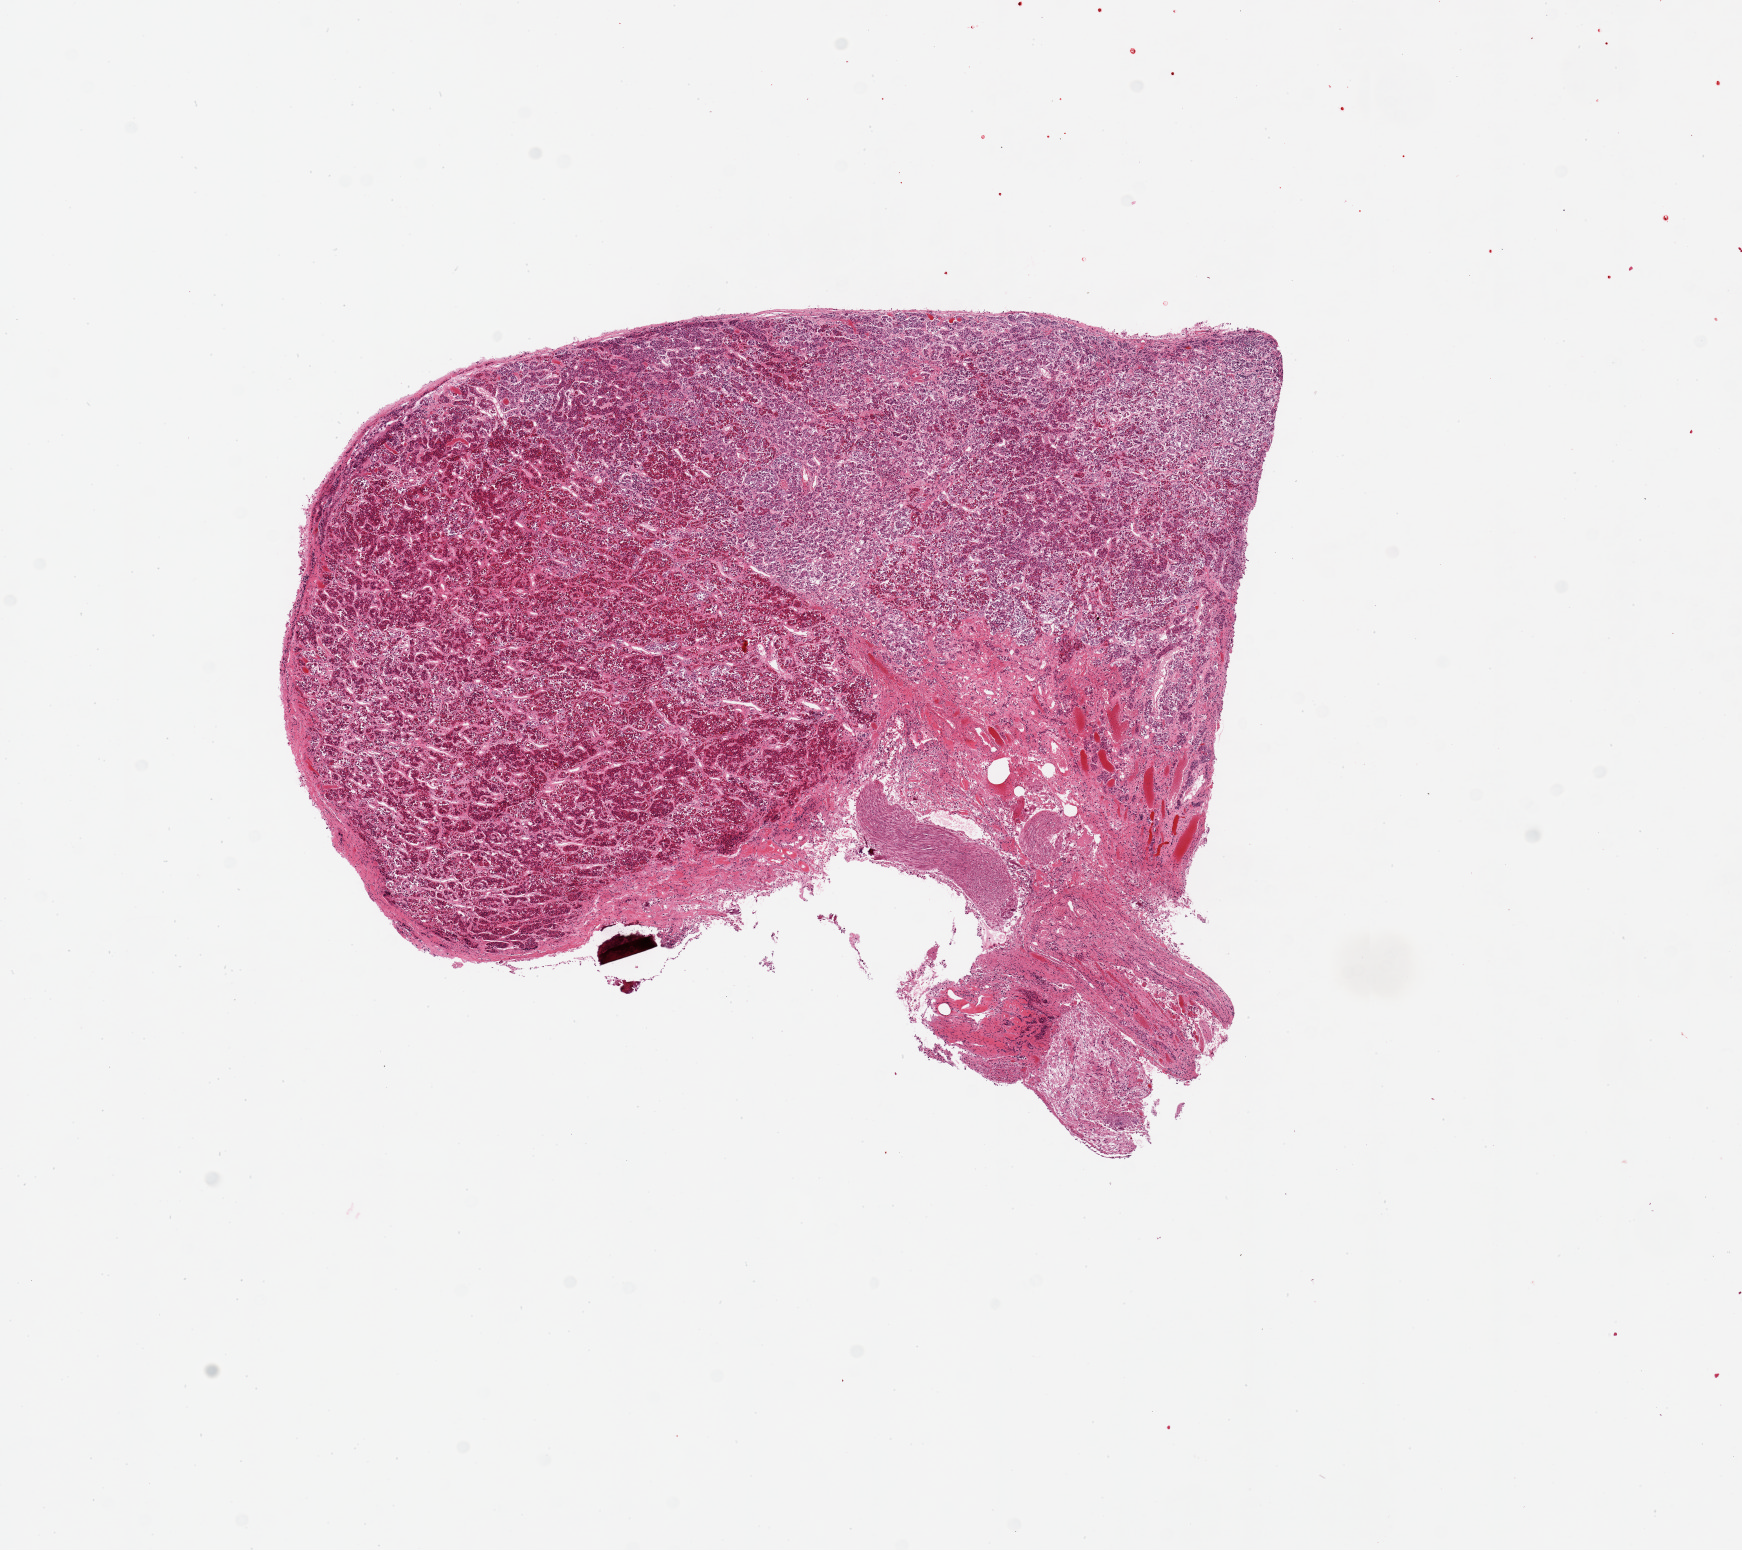
Whole-slide image, haematoxylin and eosin stain, brightfield — low-resolution overview of the scanned area, about 13.8 x 12.3 mm, PAXgene-fixed, paraffin-embedded tissue, sampled site (target tissue): pituitary, donor tissue sample. Donor sex: male.
Review note (as recorded): 1 piece. Mostly anterior with 3 mm neurohypophysis.